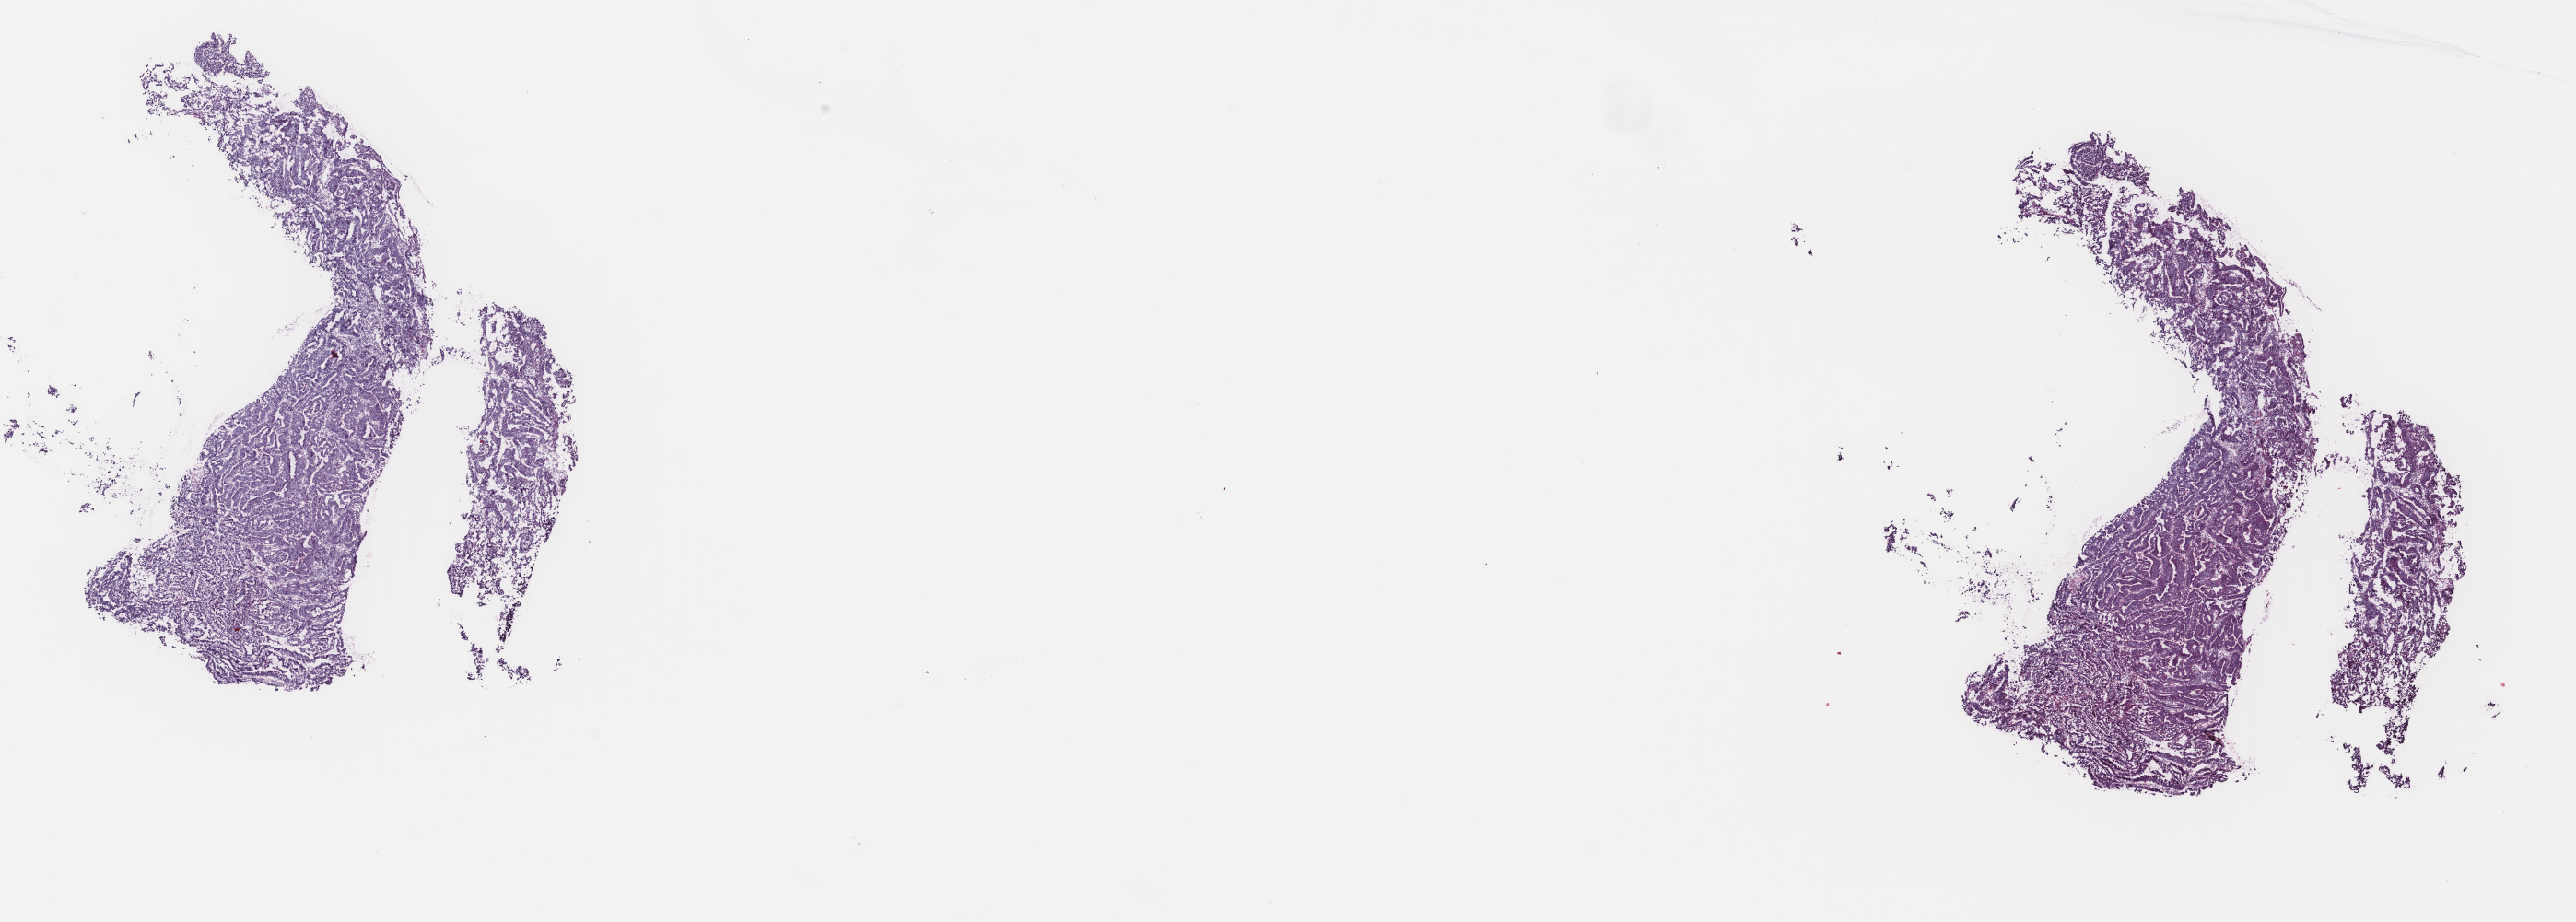
Digitized H&E-stained tissue section (whole slide) — whole scanned area (about 22.2 x 7.9 mm) shown as a low-resolution overview; frozen section; primary tumour sample from the stomach. Patient: male, age at initial diagnosis 70 years. Histologic grade: G2 (moderately differentiated). Pathologist review of this section (percent, as recorded): tumour cells 80%, tumour nuclei 80%, normal cells 0%, stromal cells 19%, necrosis 1%. Inflammatory infiltration, as recorded: lymphocyte infiltration 2%, monocyte infiltration 1%, neutrophil infiltration 3%.
Lymph nodes positive (case pathology): 0 of 22 examined. AJCC pathologic stage: IA (7th edition). Histologic diagnosis: Adenocarcinoma, NOS (cardia, NOS).